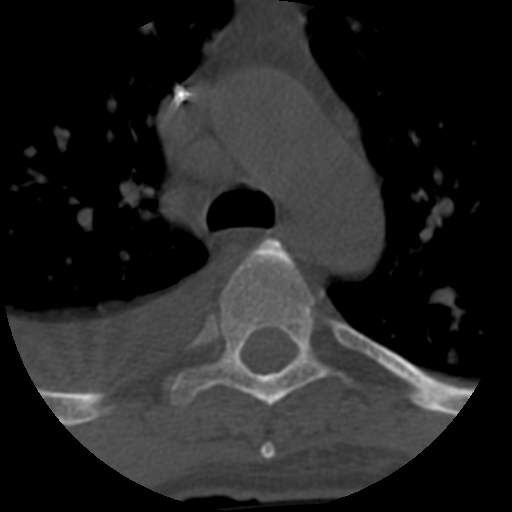
CT including the spine, one axial slice; slice 456 of 708 in the series (ordered by position); reconstruction kernel STANDARD; 120 kVp; one of 3 acquisitions stored at this slice position; bone window (W 1800 / L 400 HU); 512 × 512 image matrix, field of view 160 × 160 mm. Patient age 55 years. From the clinical record (not read from this slice): primary cancer: colon; vertebrae with lytic lesions (as recorded): T12, L1, L5.
Annotated regions visible in this slice (semi-automatically segmented with operator editing):
- T4 vertebra: bounding box <260,443,276,459> (left, top, right, bottom; pixels)
- T5 vertebra: <169,238,326,407>